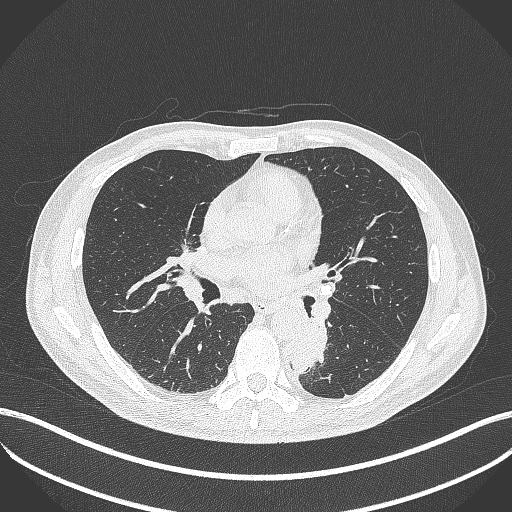
Chest CT, one axial slice. Position 214 of 451 along the scan axis. Lung window (W 1500 / L -600 HU). 1 mm slice thickness. 512 × 512 image matrix, field of view 400 × 400 mm. Patient: male, 72 years. Case-level facts recorded for this patient, not image findings: clinical TNM (as recorded): T2b N0 M1.
Outlined on this slice (rectangle marked by the reading radiologist):
- lung tumour (recorded histology: adenocarcinoma): box from (x=283, y=318) to (x=338, y=373) px